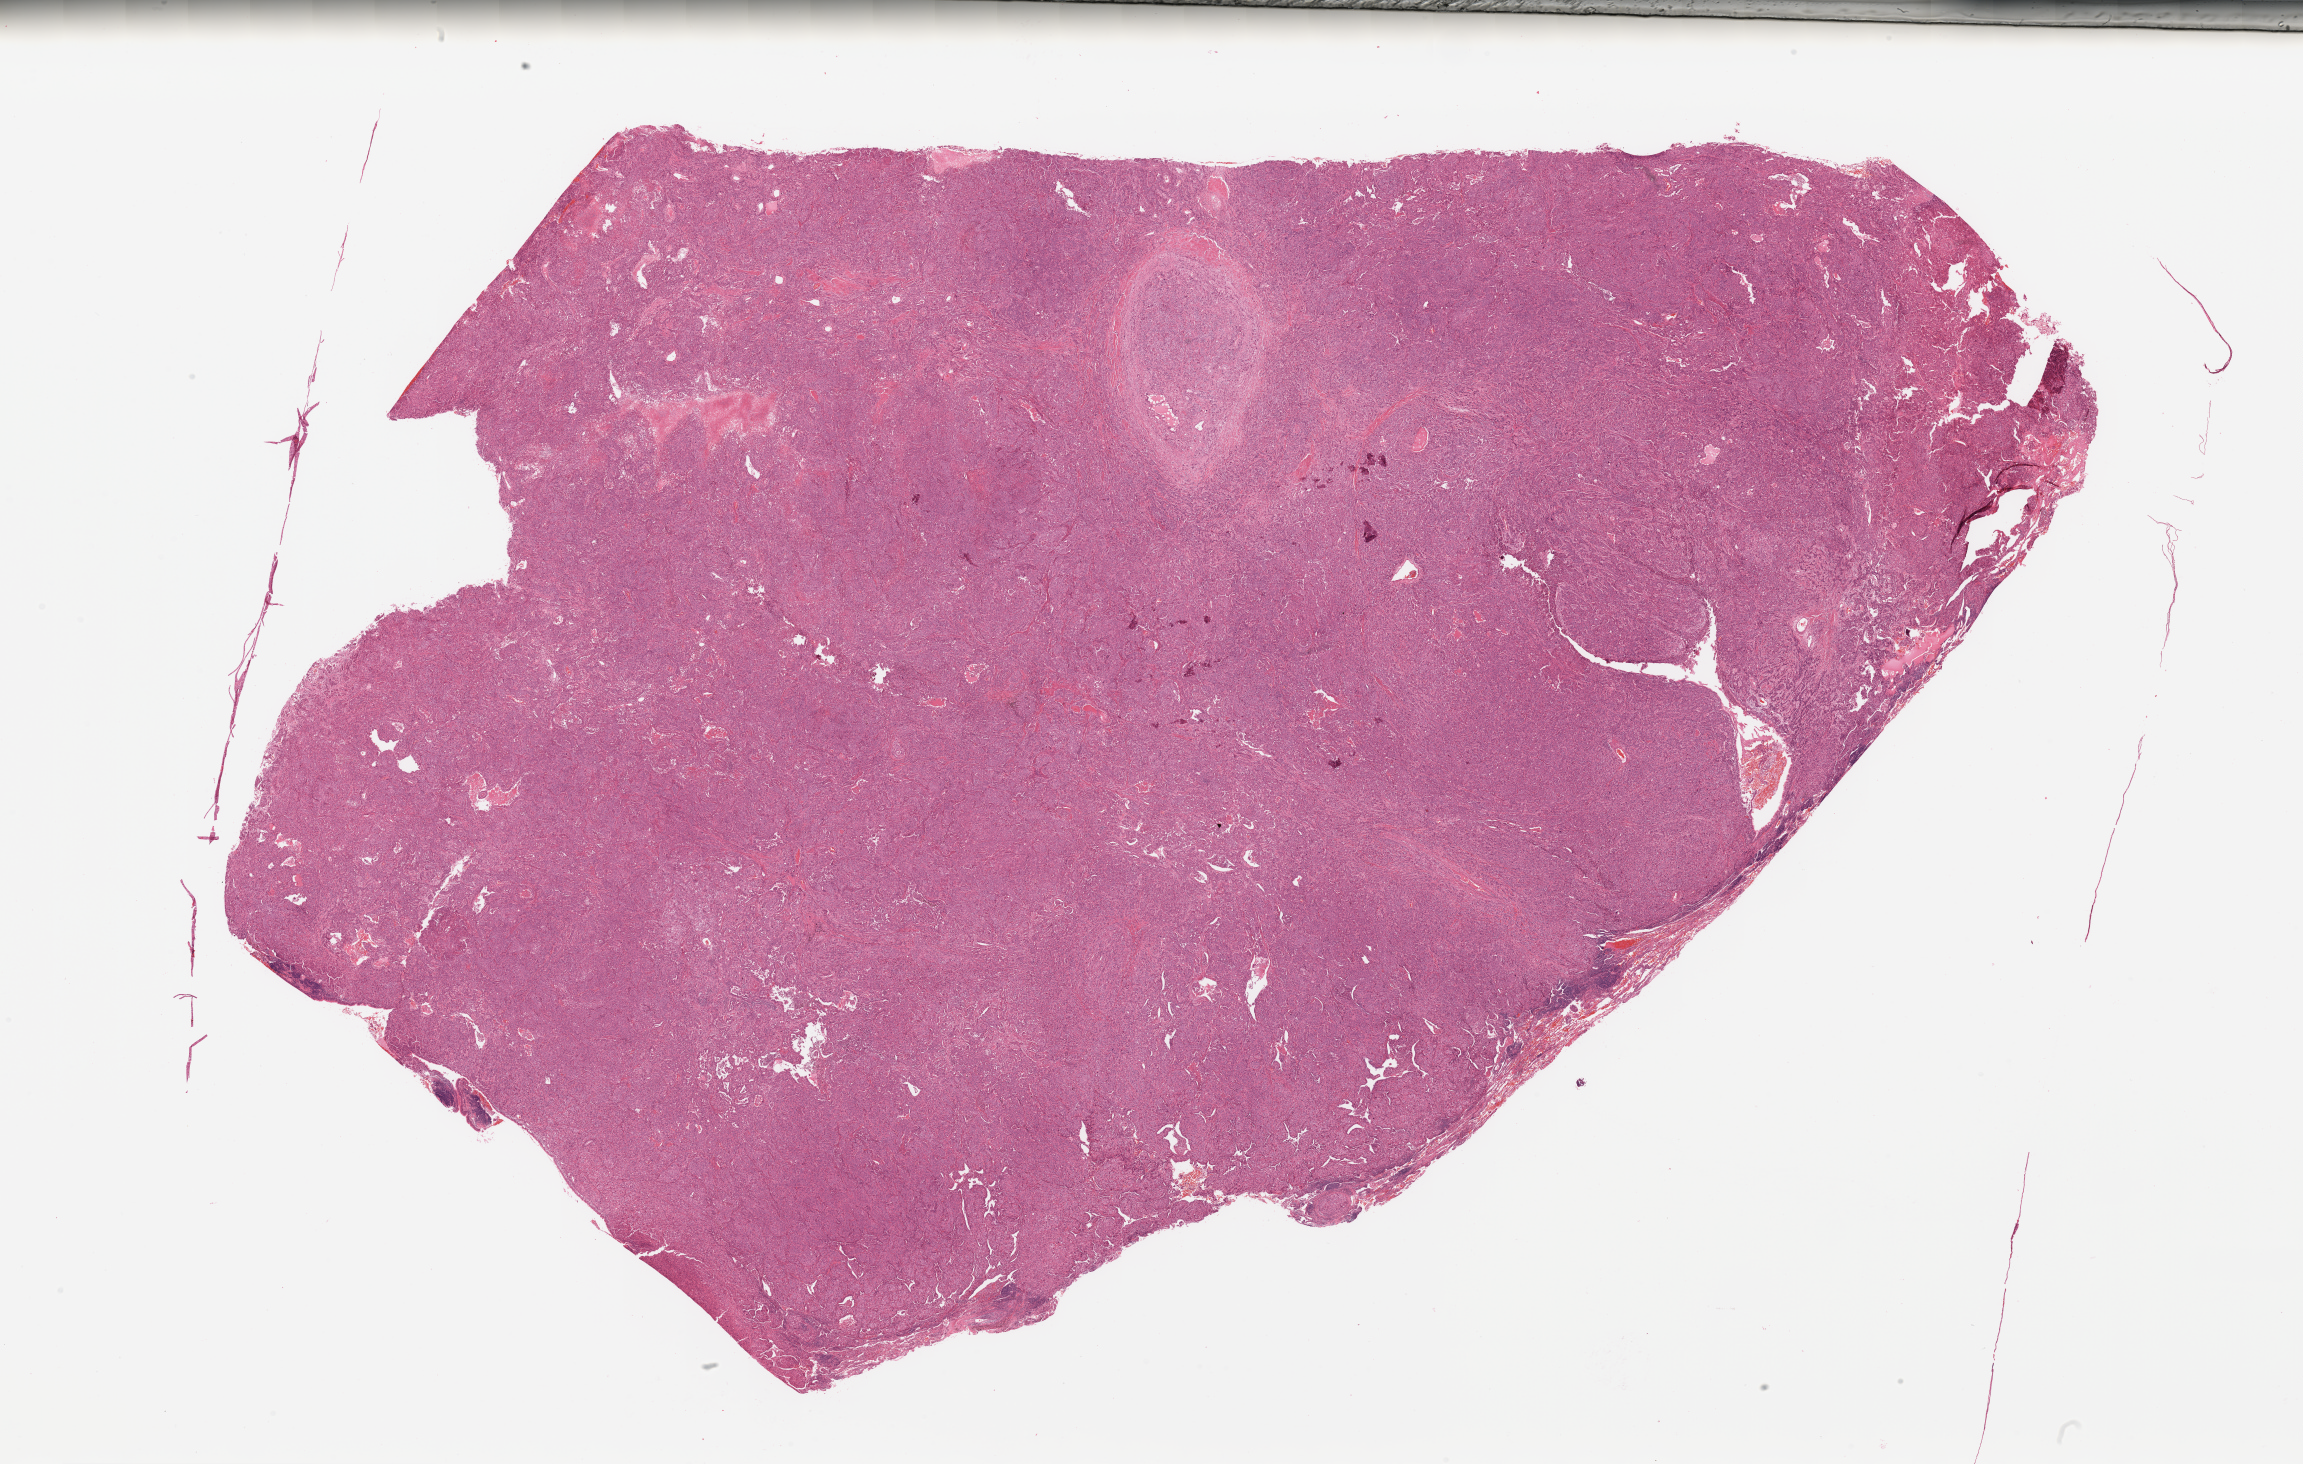
H&E-stained whole-slide image, whole scanned area (about 36.4 x 23.2 mm, acquisition: 20x scan) shown as a low-resolution overview; lung, tissue type not recorded.
* patient diagnosis (cohort enrolment): lung adenocarcinoma (lung)